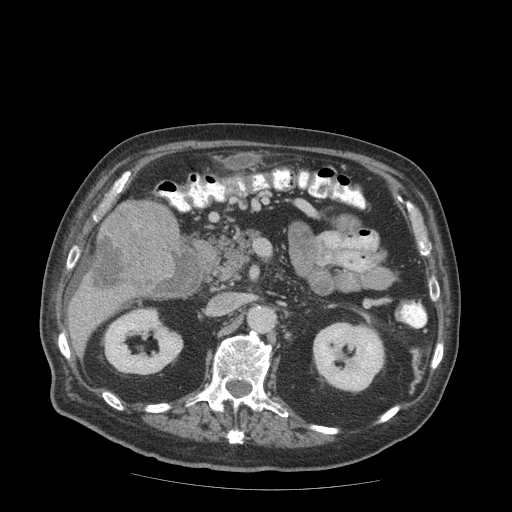
Contrast-enhanced abdominal CT (liver protocol), one axial slice; slice 31 of 99 in the series (ordered by position); reconstruction kernel STANDARD; 140 kVp; soft-tissue window (W 400 / L 40 HU); 512 × 512 image matrix, field of view 420 × 420 mm. From the clinical record (not read from this slice): diagnosis: hepatocellular carcinoma (patient treated with transarterial chemoembolisation; whether this scan precedes or follows treatment is not stated here); TNM stage (as recorded): Stage-IIIB.
Outlined on this slice (semi-automatically segmented with operator editing):
- liver parenchyma outside the tumour (the mass and vessels are separate outlines, so this box may not span the whole liver): bounding box (x1, y1, x2, y2) in pixels: (68, 202, 184, 348)
- mass: (91, 199, 181, 295)